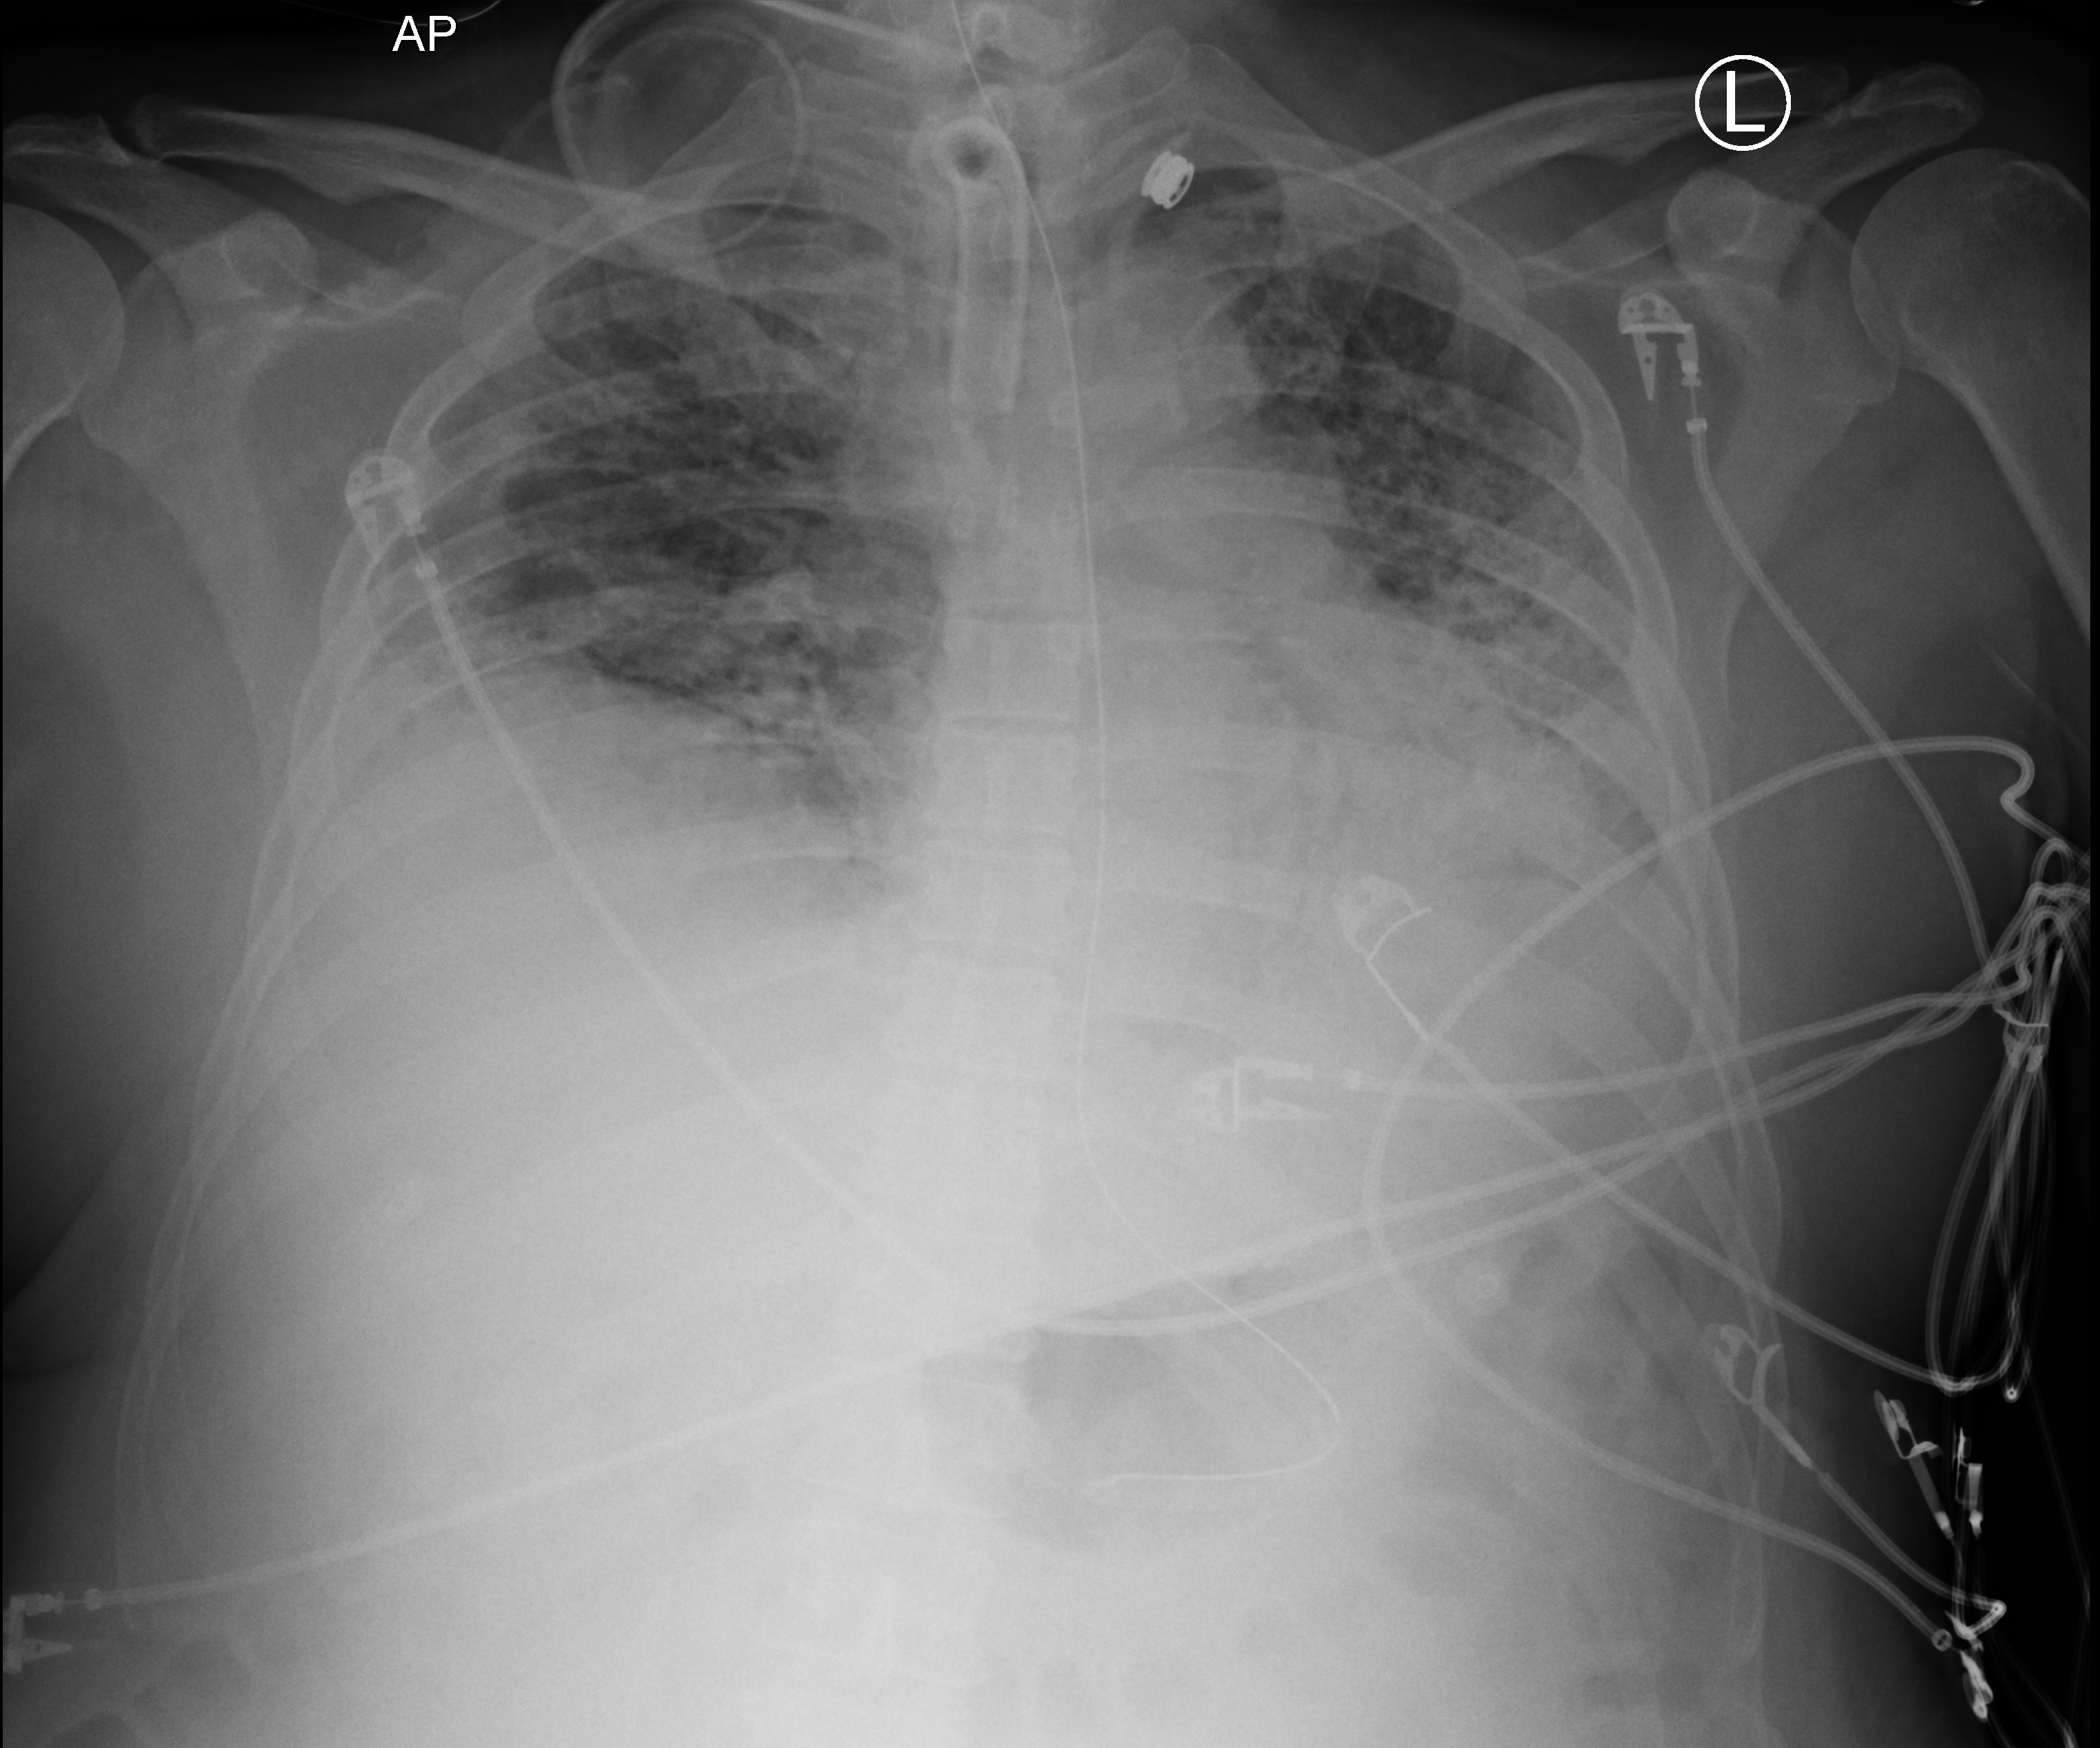
Chest X-ray (portable); anteroposterior (AP) projection. Male patient hospitalised with COVID-19, age 18–59 years.
Hospital-stay facts (about this admission, not read from this image; timing relative to this image not recorded):
- mechanically ventilated during this hospital stay: yes
- chronic kidney disease (admission record): no
- admitted to intensive care during this hospital stay: yes